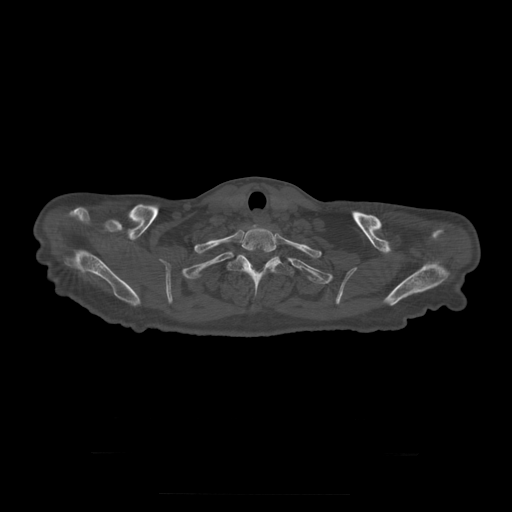
CT including the spine, one axial slice; slice 280 of 397 in the series (ordered by position); 120 kVp; bone window (W 1800 / L 400 HU); 1.25 mm slice thickness; 512 × 512 image matrix, field of view 510 × 510 mm. Patient age 73 years. From the clinical record (not read from this slice): primary cancer: prostate.
Outlined on this slice (semi-automatically segmented with operator editing):
- T1 vertebra: bounding box <238,231,276,253> (left, top, right, bottom; pixels)
- T2 vertebra: <228,255,295,298>